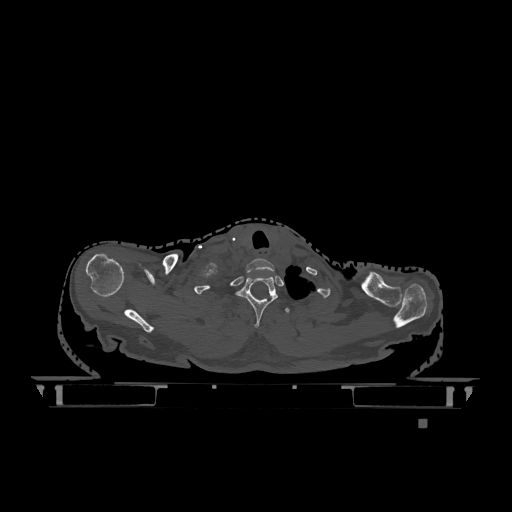
CT including the spine, one axial slice. Slice 997 of 1317 in the series (ordered by position). Bone window (W 1800 / L 400 HU). 0.5 mm slice thickness. 512 × 512 image matrix. Patient: female, 74 years. From the clinical record (not read from this slice): primary cancer: lung.
Outlined on this slice (semi-automatic segmentation, software-assisted and operator-edited):
- T1 vertebra: box from (x=236, y=276) to (x=278, y=327) px
- T2 vertebra: (x=285, y=308)–(x=290, y=313)